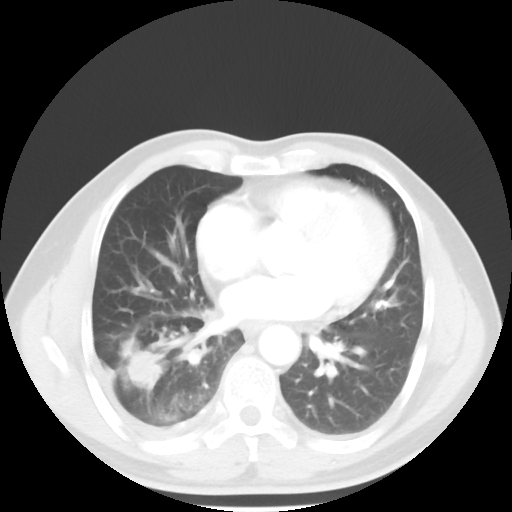
Chest CT, one axial slice. Position 24 of 56 along the scan axis. Lung window (W 1500 / L -600 HU). 512 × 512 image matrix, field of view 344 × 344 mm. Male patient, age 56 years. Case-level facts recorded for this patient, not image findings: clinical TNM (as recorded): T2 N3 M1.
Annotated regions visible in this slice (bounding box drawn by a radiologist):
- lung tumour (recorded histology: adenocarcinoma): box from (x=127, y=349) to (x=167, y=395) px